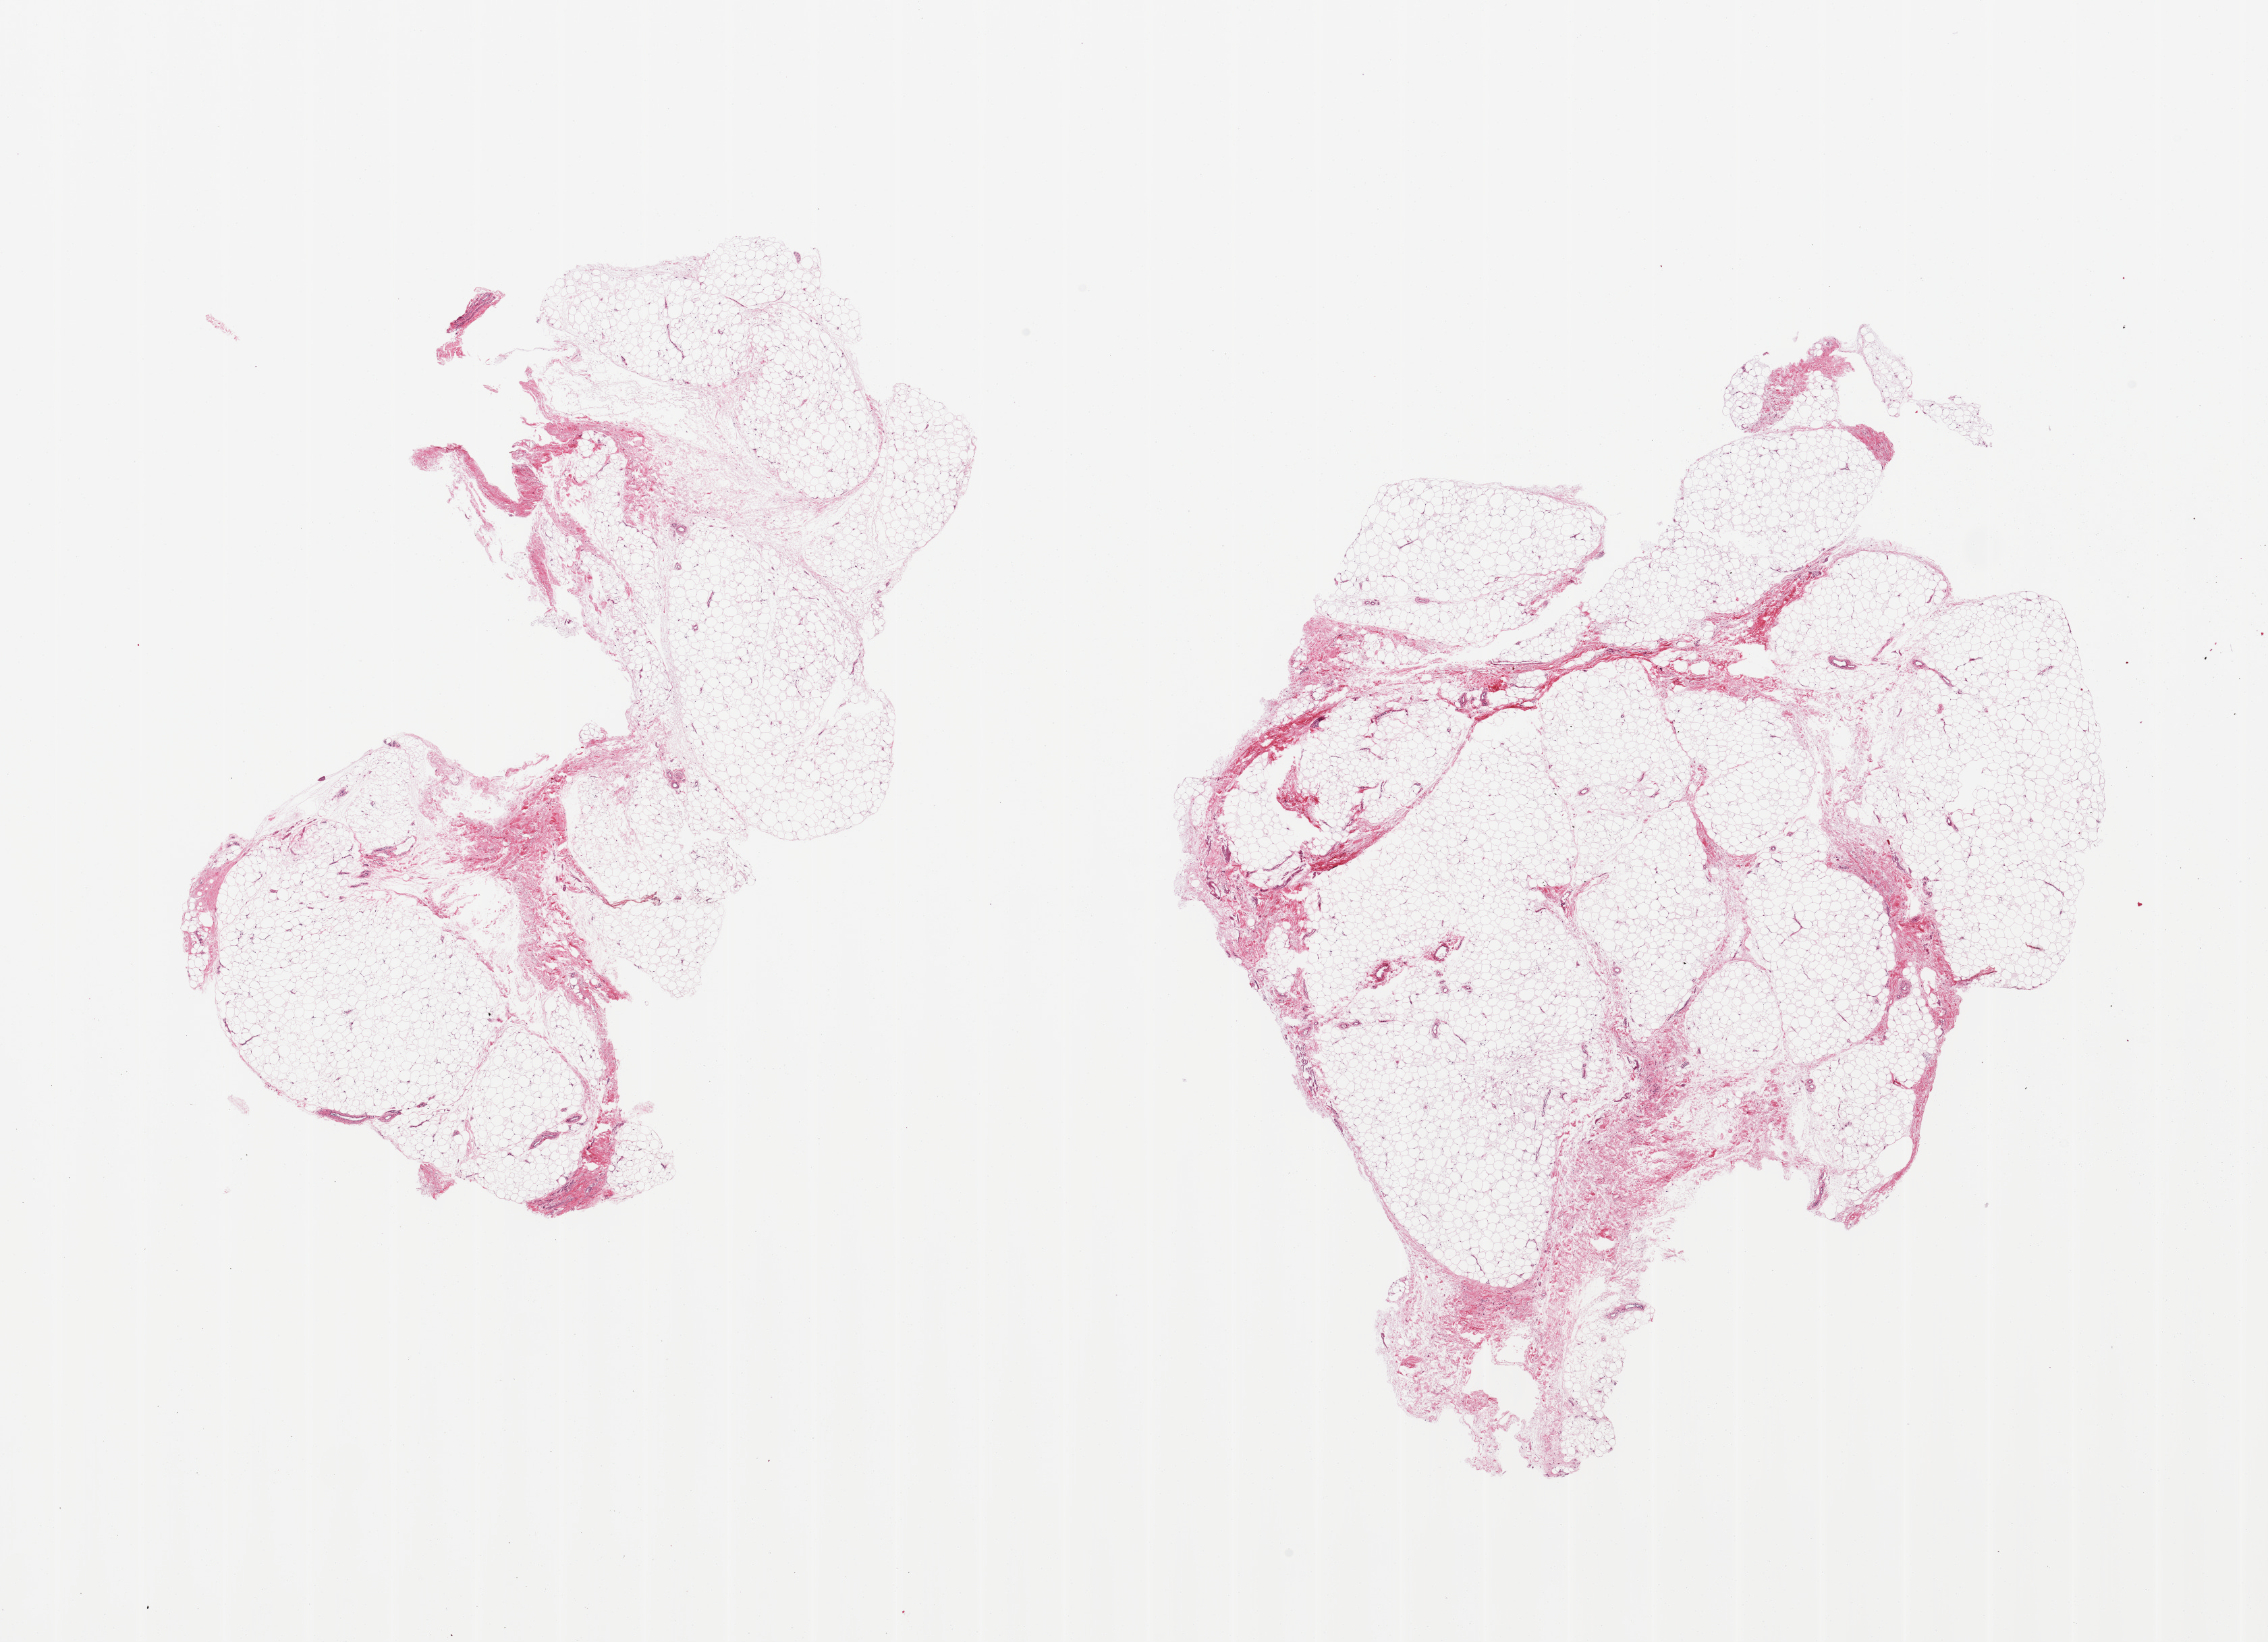
Haematoxylin and eosin whole-slide image, a low-resolution overview of the entire scanned area, about 26.6 x 19.2 mm, PAXgene-fixed, paraffin-embedded tissue, target tissue: adipose tissue, donor tissue sample. Donor: male.
Pathologist's review note for this sample: 2 pieces; <10% fibrous content.